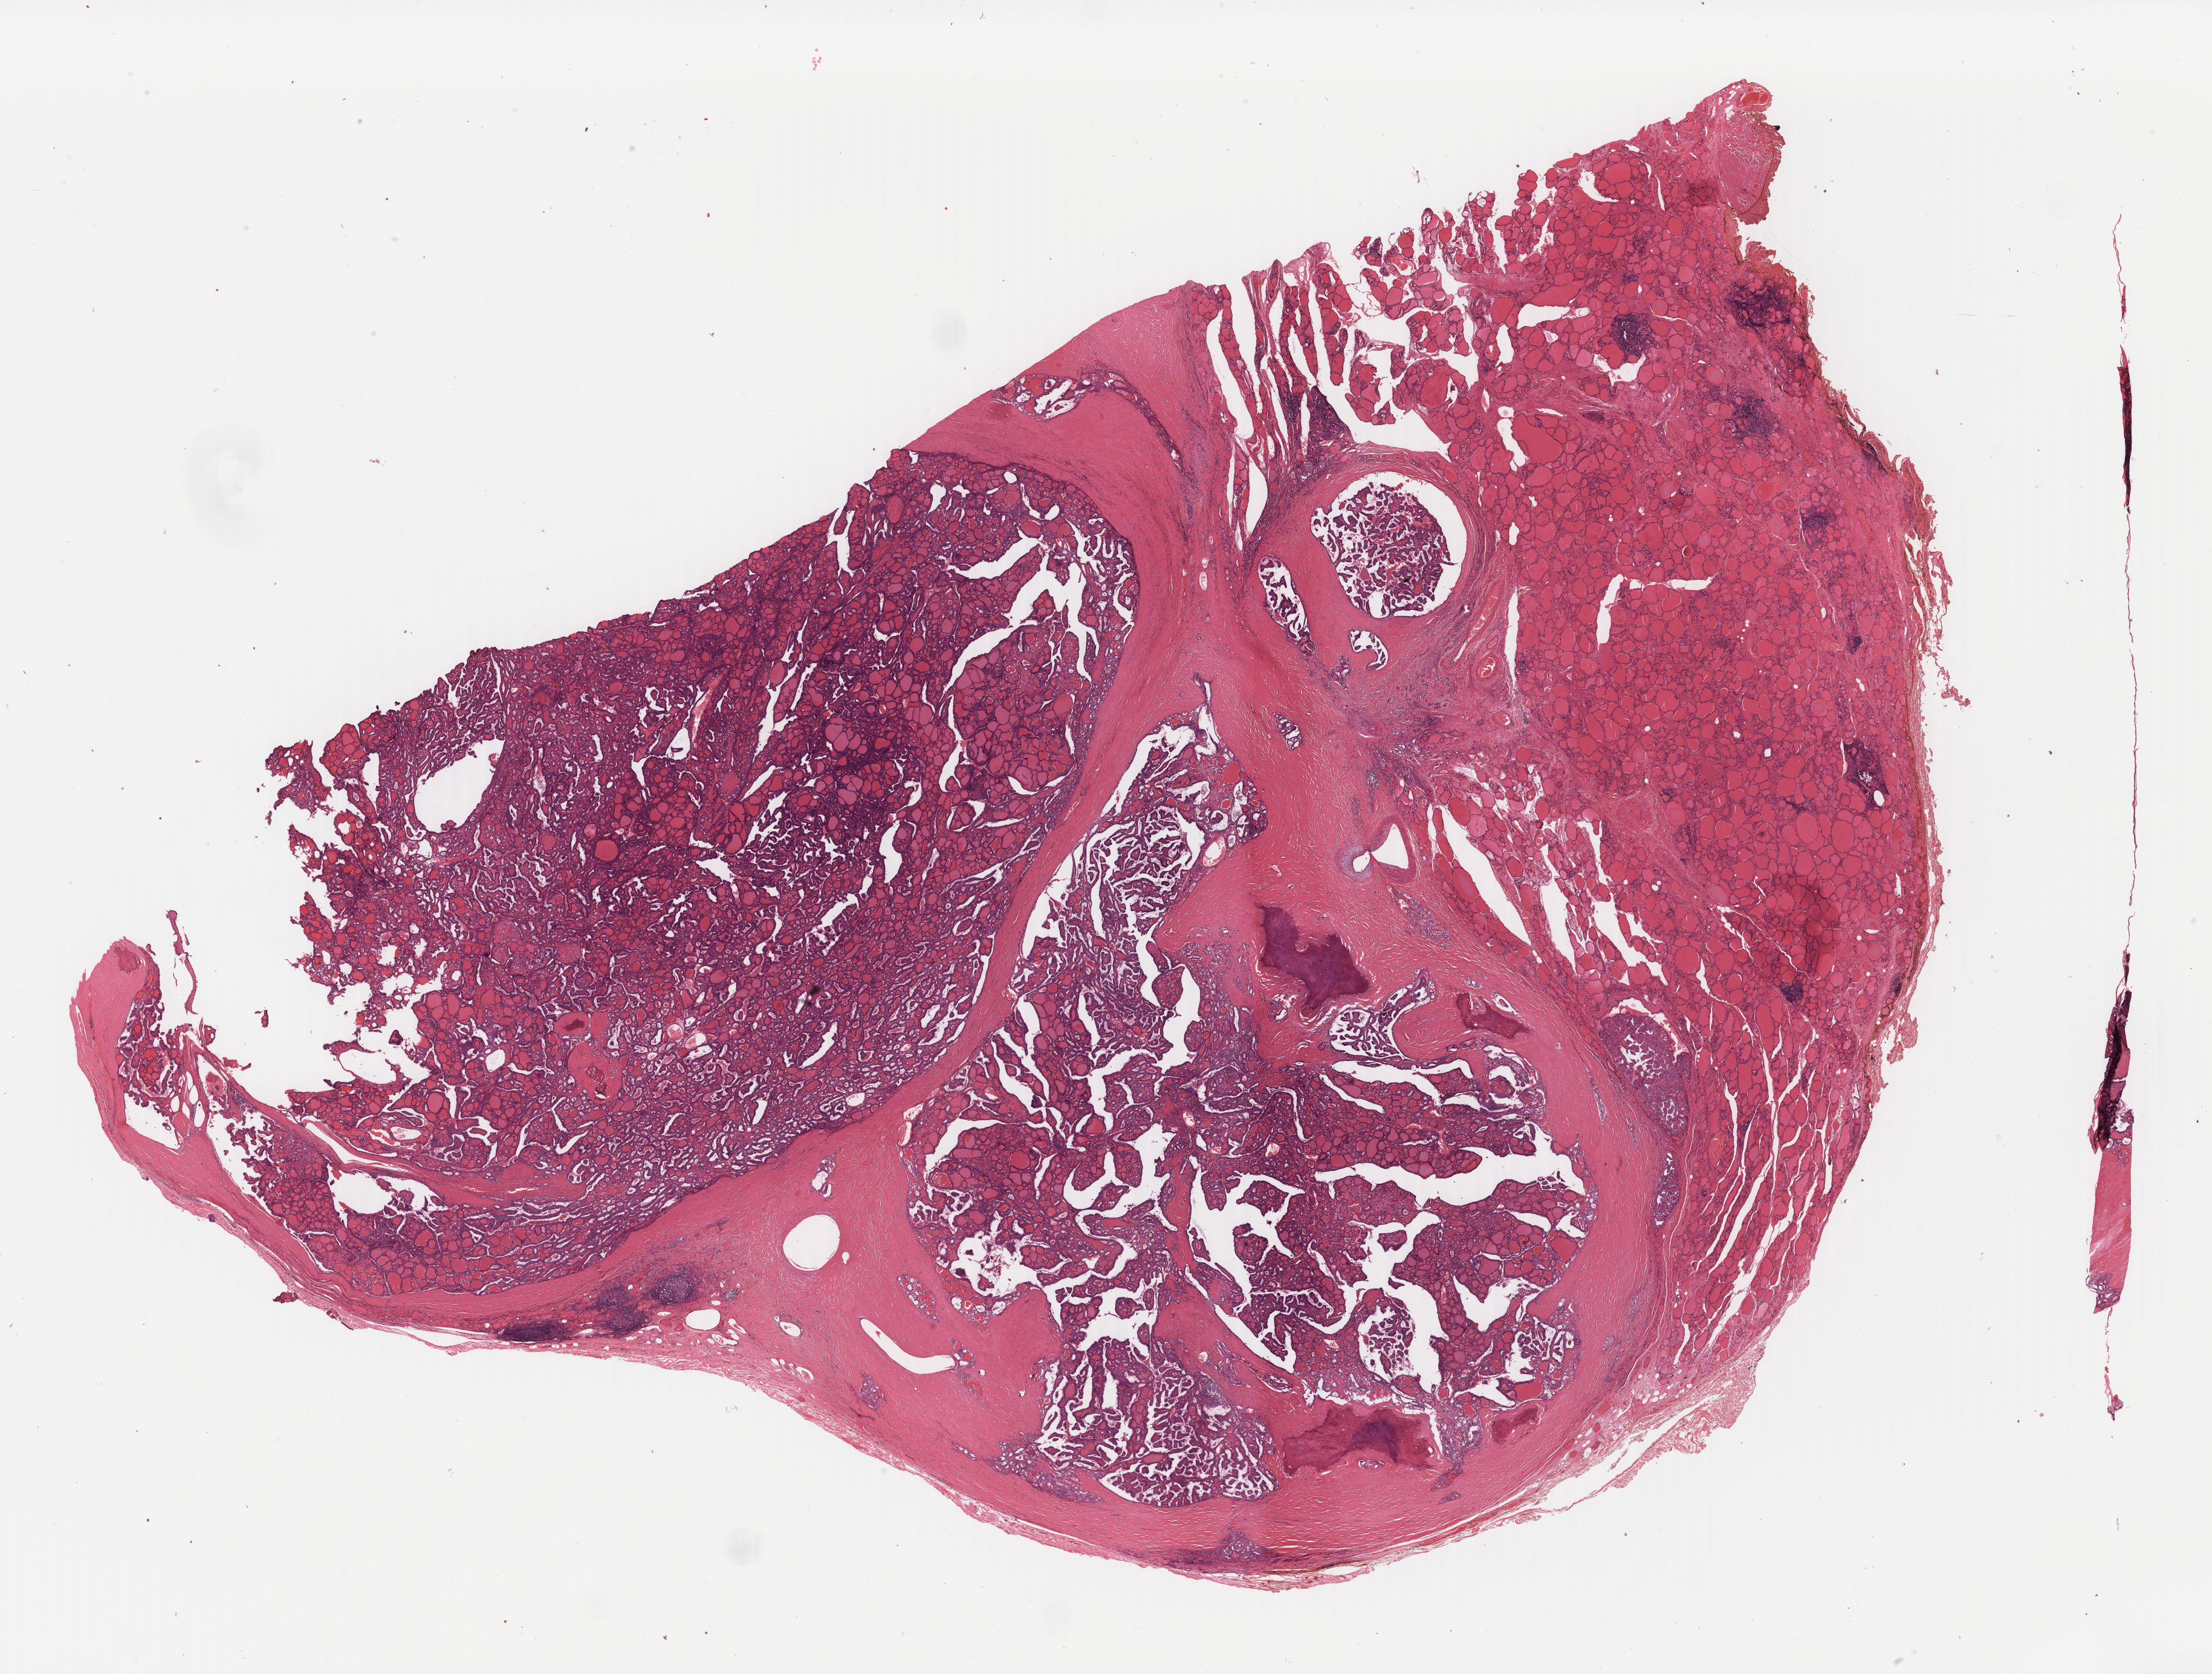
Whole-slide histology image, Hematoxylin and eosin (H&E) stained — shown as a low-resolution overview of the whole scanned area (about 29.0 x 22.0 mm, from a 40x scan), formalin-fixed paraffin-embedded (FFPE) diagnostic section, primary tumour sample from the thyroid. Male, age 31 years at initial diagnosis.
Histologic diagnosis: Papillary adenocarcinoma, NOS (thyroid gland). TNM: T3 N1a M0. AJCC pathologic stage: I (7th edition).